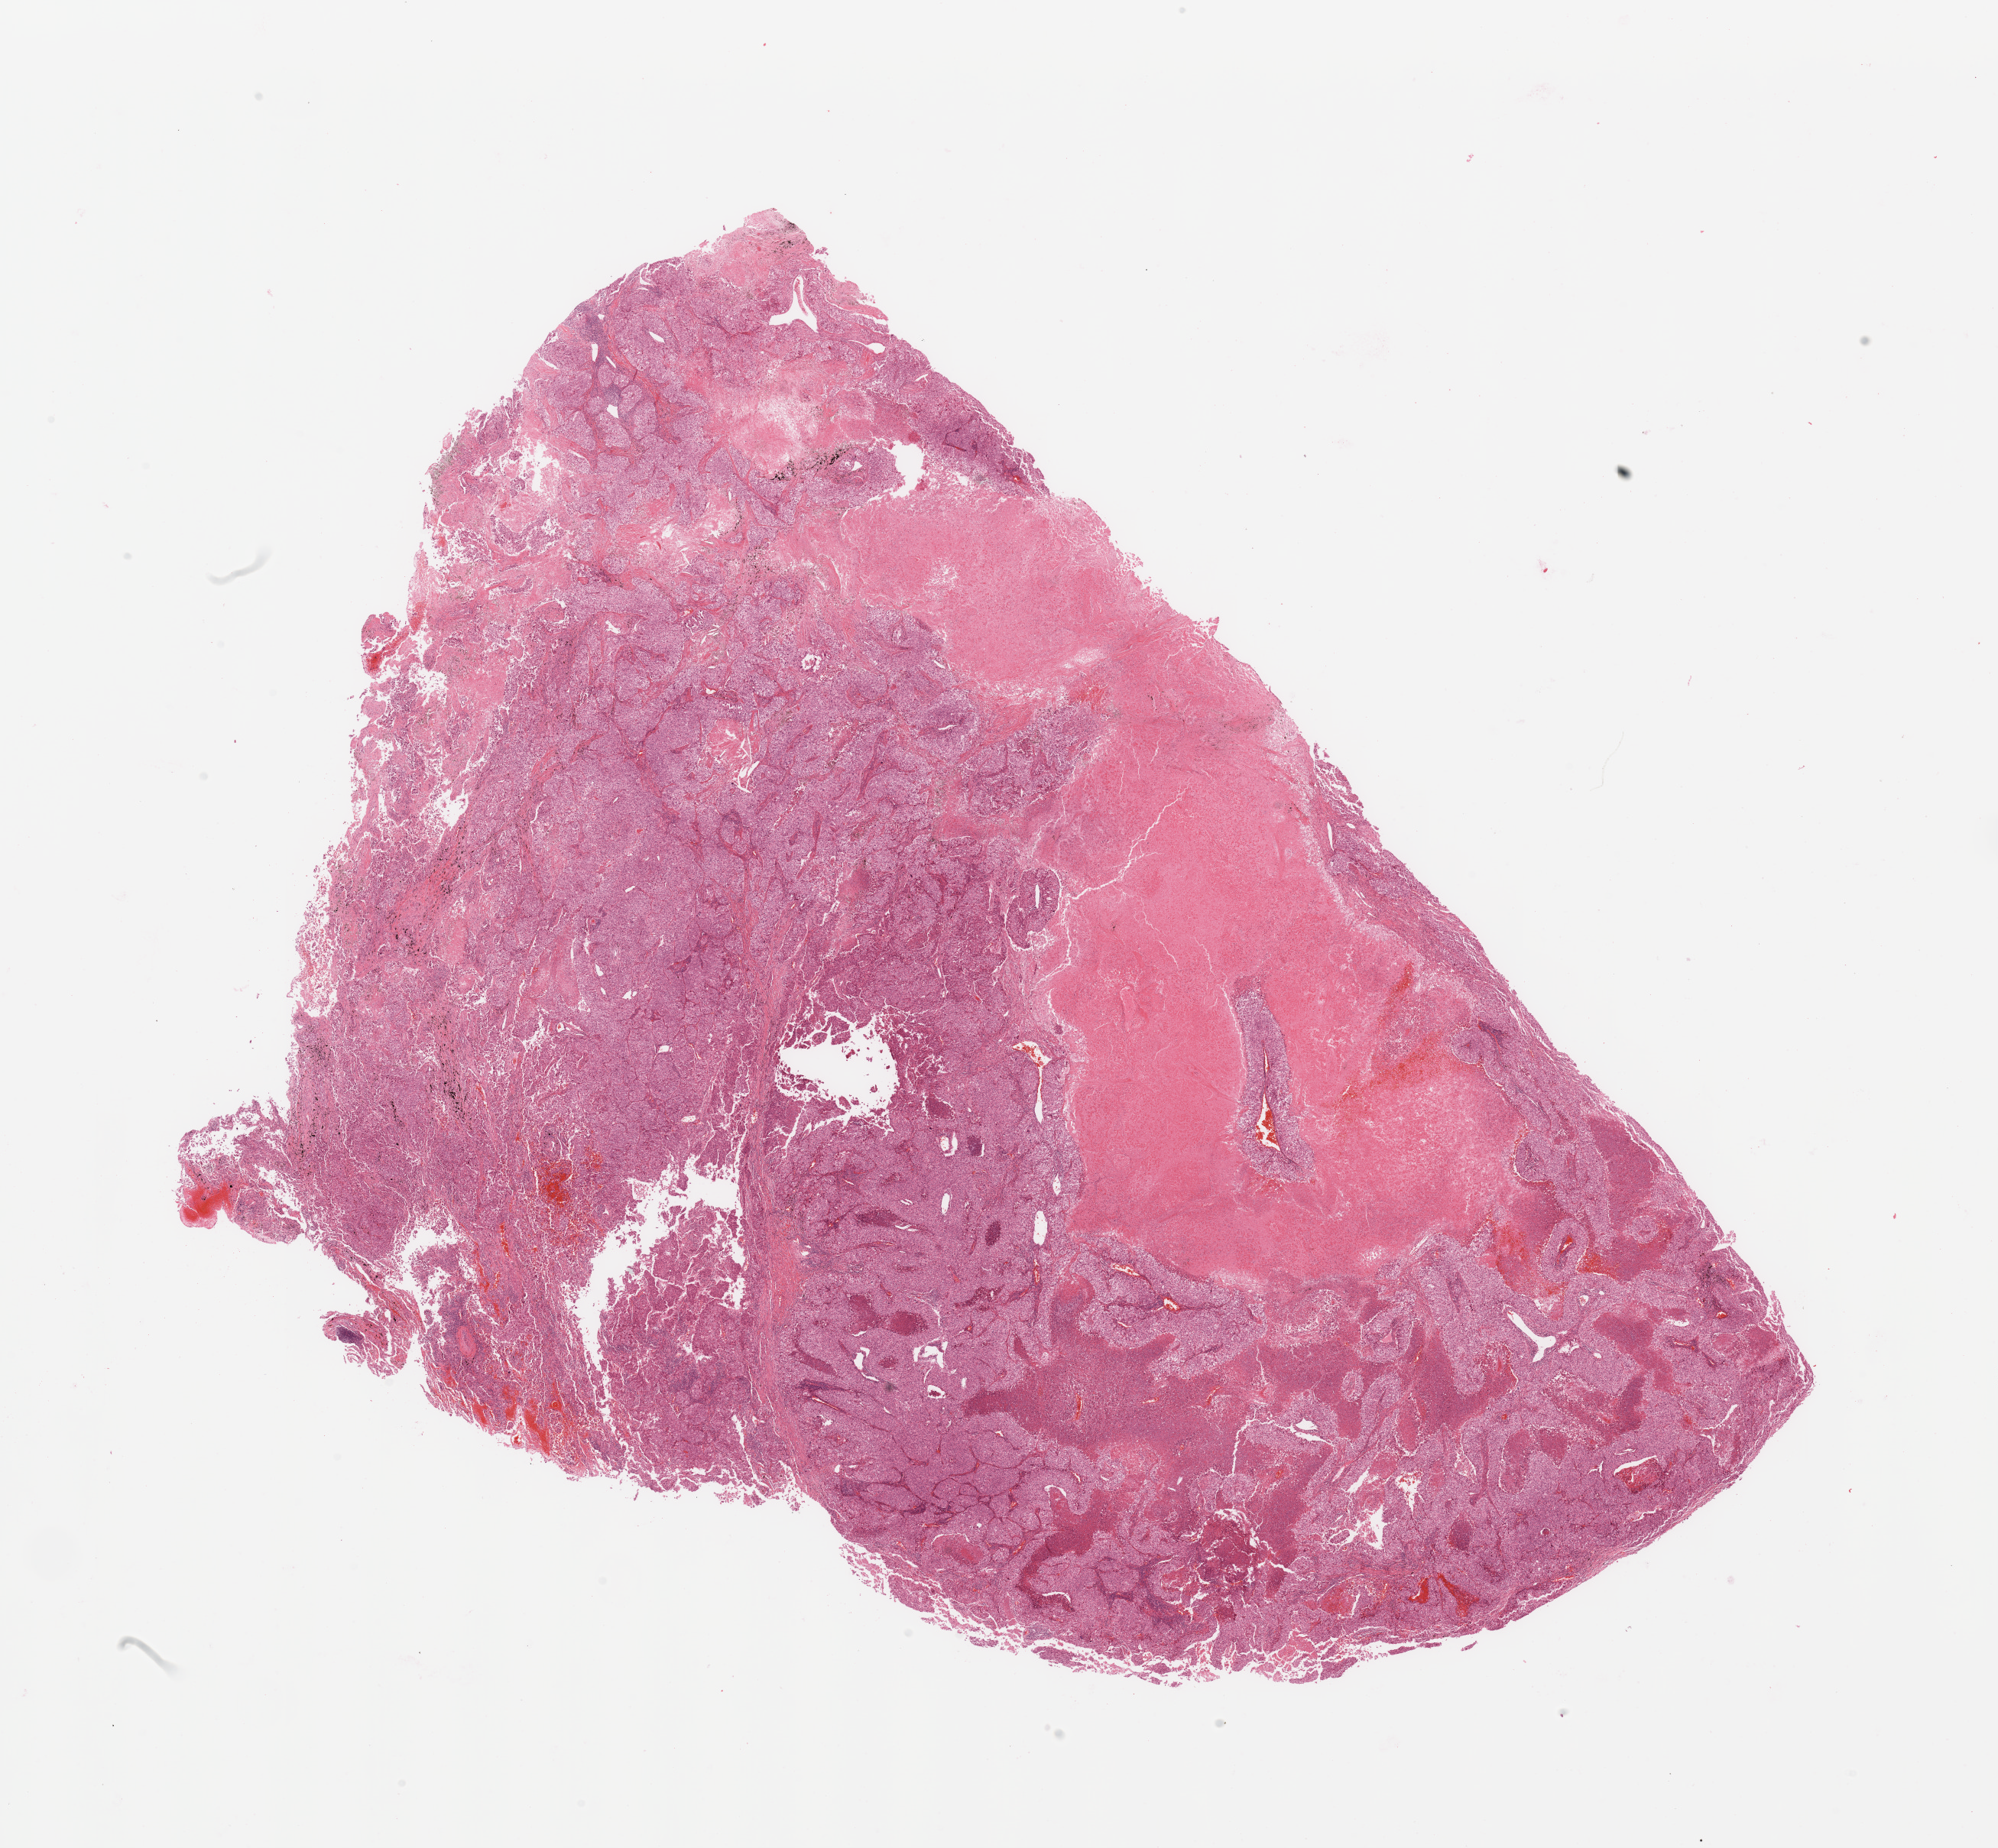
Digitized Hematoxylin and eosin (H&E) stained tissue section (whole slide), whole scanned area (about 20.7 x 19.1 mm) shown as a low-resolution overview; tumour tissue sample, lung. 59-year-old male patient. Histologic grade: G3 (poorly differentiated).
Diagnosis: Adenocarcinoma, NOS. Primary tumour site (as recorded): right upper lobe. AJCC pathologic stage: IB.